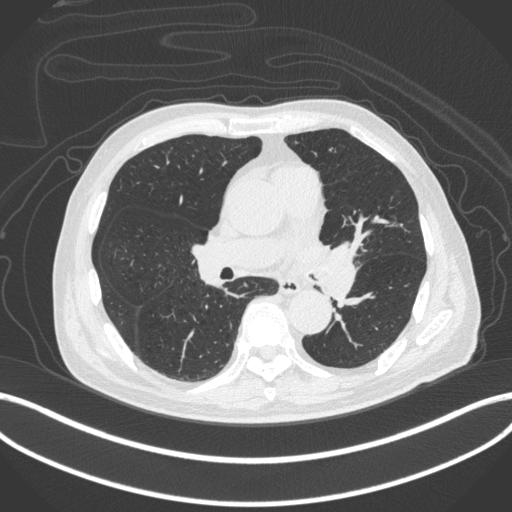
Chest CT, one axial slice; slice 231 of 420 in the series (ordered by position); lung window (W 1500 / L -600 HU); 1 mm slice thickness; 512 × 512 image matrix, field of view 400 × 400 mm. Patient: male, 77 years. From the clinical record (not read from this slice): clinical TNM (as recorded): T3 N1 M0.
Outlined on this slice (bounding box drawn by a radiologist):
- lung tumour (recorded histology: adenocarcinoma): bounding box <310,235,354,307> (left, top, right, bottom; pixels)